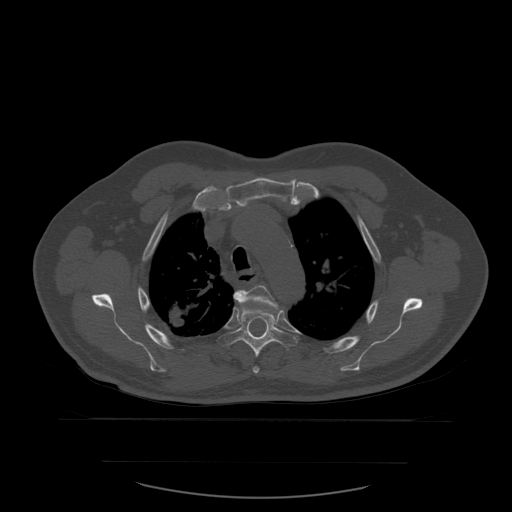
CT including the spine, one axial slice. Slice 429 of 590 in the series (ordered by position). Bone window (W 1800 / L 400 HU). 1.25 mm slice thickness. 512 × 512 image matrix, field of view 479 × 479 mm. Patient age 71 years. Case-level facts recorded for this patient, not image findings: primary cancer: lung; vertebrae with lytic lesions (as recorded): T1, T2, L5, S1.
Structures marked on this image (semi-automatically segmented with operator editing):
- T4 vertebra: bounding box (x1, y1, x2, y2) in pixels: (235, 286, 279, 374)
- T5 vertebra: (218, 294, 298, 358)